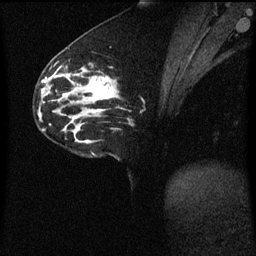
Breast MRI (dynamic contrast-enhanced), one sagittal slice. Position 25 of 60 along the scan axis. Dynamic contrast-enhanced series, image 2 of 3 at this slice position (ordered by acquisition). 1.5 T. TE 4.2 ms, TR 8.4 ms. 2 mm slice thickness. 256 × 256 image matrix. Patient: female, 33 years. Case-level facts recorded for this patient, not image findings: setting: breast cancer imaged before/during neoadjuvant chemotherapy; receptor status: triple-negative.
Annotated regions visible in this slice (semi-automatic segmentation, software-assisted and operator-edited):
- analysis volume of interest (the breast-tissue region the enhancement analysis was run in; not a lesion): box from (x=76, y=68) to (x=123, y=113) px
- tumour enhancement mask (voxels above the 70 % enhancement threshold inside the analysis volume of interest): (x=84, y=76)–(x=113, y=101)